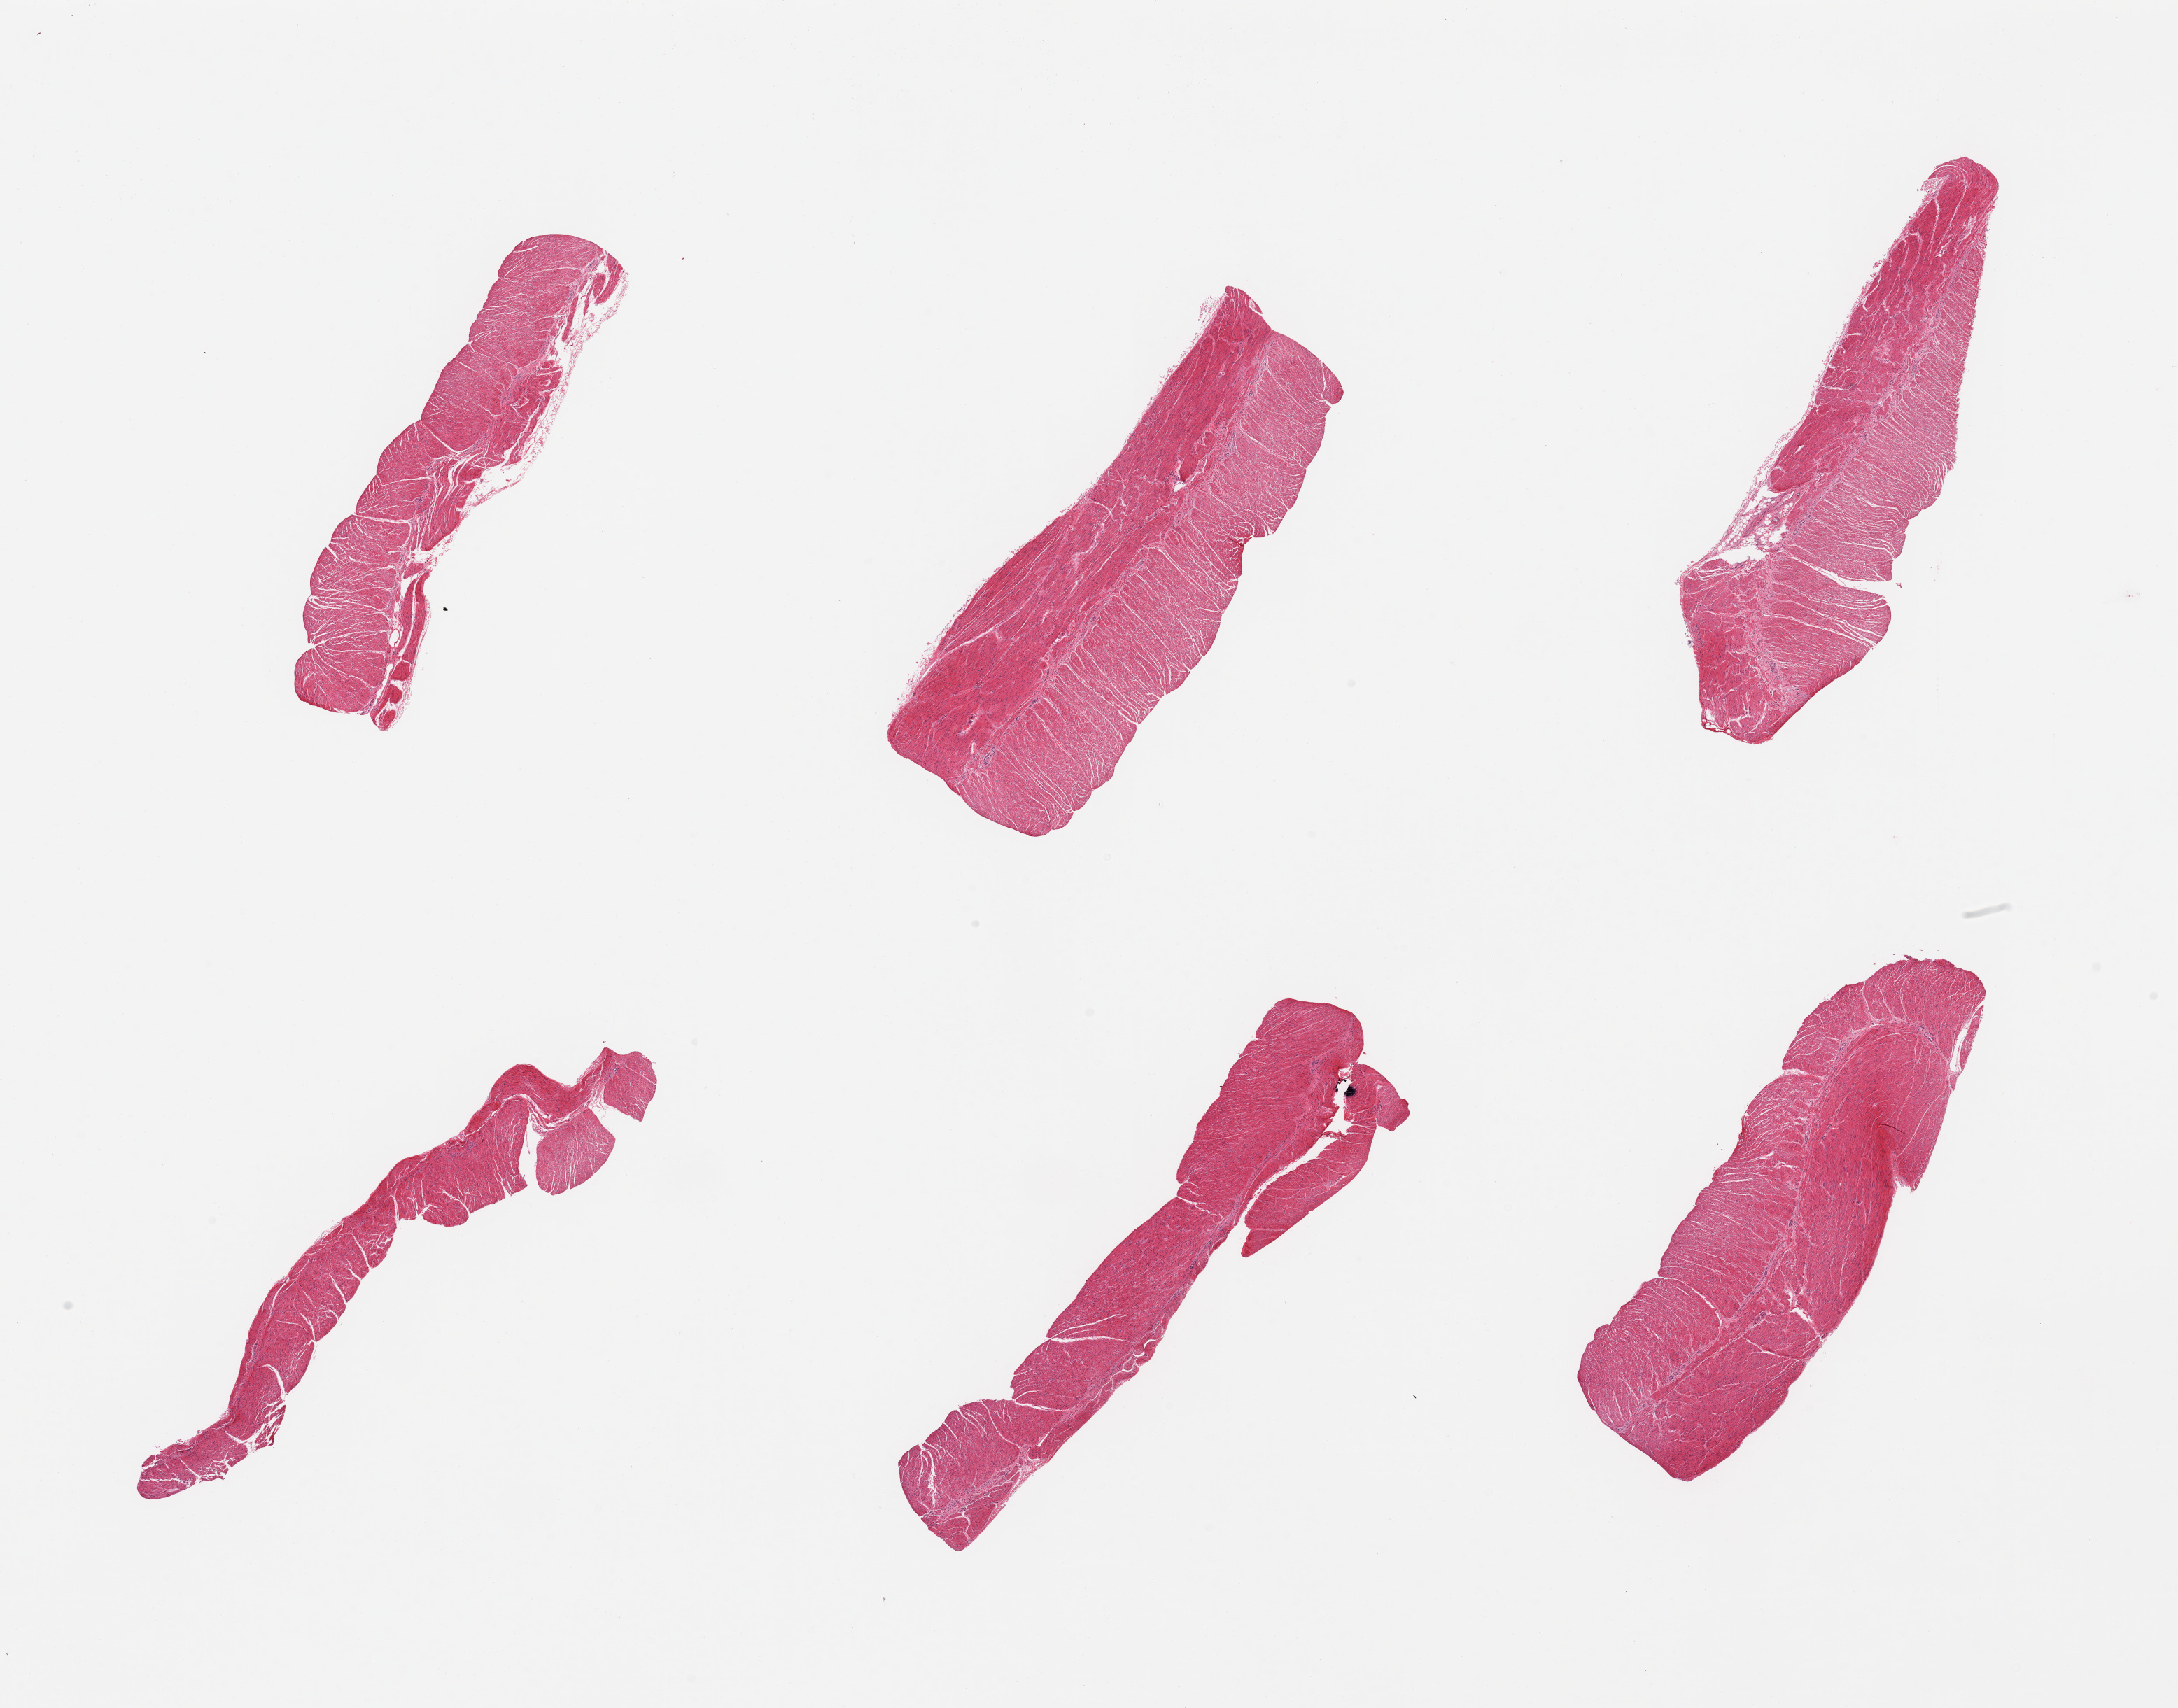
Digitized H&E-stained section — a low-resolution overview of the entire scanned area, about 24.6 x 19.3 mm (acquisition: 20x scan). PAXgene-fixed paraffin-embedded (PFPE) section. Section of sigmoid colon (target tissue). Donor tissue sample.
- review note (as recorded): 6 pieces, confirmed target muscularis